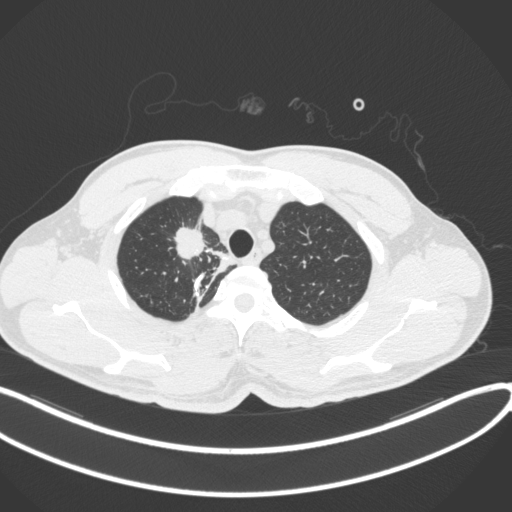
Chest CT, one axial slice; slice 320 of 391 in the series (ordered by position); reconstruction kernel B31f; 120 kVp; lung window (W 1500 / L -600 HU); 1 mm slice thickness; 512 × 512 image matrix. Male patient, age 48 years. From the clinical record (not read from this slice): clinical TNM (as recorded): T1c N1 M1.
Annotated regions visible in this slice (bounding box drawn by a radiologist):
- lung tumour (recorded histology: adenocarcinoma): bounding box <170,221,209,264> (left, top, right, bottom; pixels)